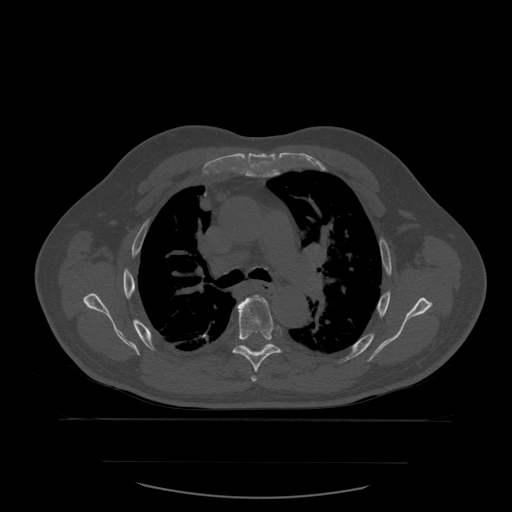
CT including the spine, one axial slice; slice 405 of 590 in the series (ordered by position); bone window (W 1800 / L 400 HU); 1.25 mm slice thickness; 512 × 512 image matrix, field of view 479 × 479 mm. Patient age 71 years. Case-level facts recorded for this patient, not image findings: primary cancer: lung; vertebrae with lytic lesions (as recorded): T1, T2, L5, S1.
Structures marked on this image (semi-automatic segmentation, software-assisted and operator-edited):
- T5 vertebra: bounding box (x1, y1, x2, y2) in pixels: (251, 376, 258, 382)
- T6 vertebra: (233, 296, 282, 373)
- T7 vertebra: (244, 344, 273, 352)